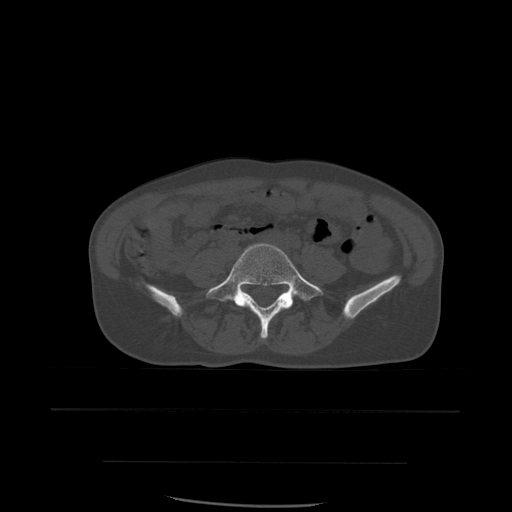
CT including the spine, one axial slice; position 150 of 574 along the scan axis; bone window (W 1800 / L 400 HU); 512 × 512 image matrix, field of view 392 × 392 mm. Patient age 48 years. From the clinical record (not read from this slice): primary cancer: lung; vertebrae with lytic lesions (as recorded): T11.
Outlined on this slice (semi-automatic segmentation, software-assisted and operator-edited):
- L5 vertebra: bounding box (x1, y1, x2, y2) in pixels: (207, 243, 324, 339)